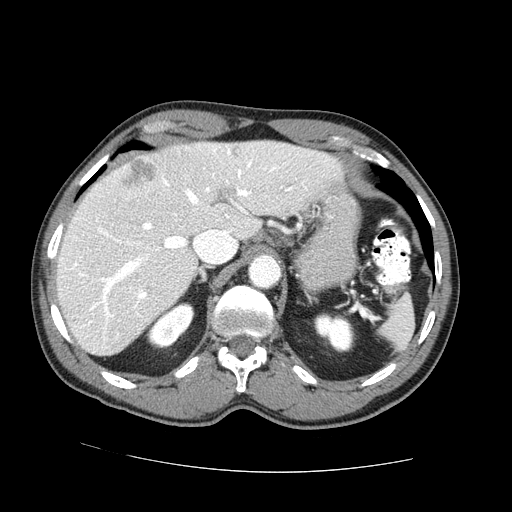
Contrast-enhanced abdominal CT (liver protocol), one axial slice; position 51 of 73 along the scan axis; one of 2 acquisitions stored at this slice position; soft-tissue window (W 400 / L 40 HU); 512 × 512 image matrix, field of view 380 × 380 mm. From the clinical record (not read from this slice): diagnosis: hepatocellular carcinoma (patient treated with transarterial chemoembolisation; whether this scan precedes or follows treatment is not stated here); TNM stage (as recorded): Stage-IVA; Child-Pugh class: A; tumour differentiation: no biopsy.
Outlined on this slice (semi-automatic segmentation, software-assisted and operator-edited):
- liver parenchyma outside the tumour (the mass and vessels are separate outlines, so this box may not span the whole liver): bounding box (x1, y1, x2, y2) in pixels: (56, 140, 344, 356)
- mass: (122, 159, 155, 189)
- liver vessels: (72, 148, 307, 325)